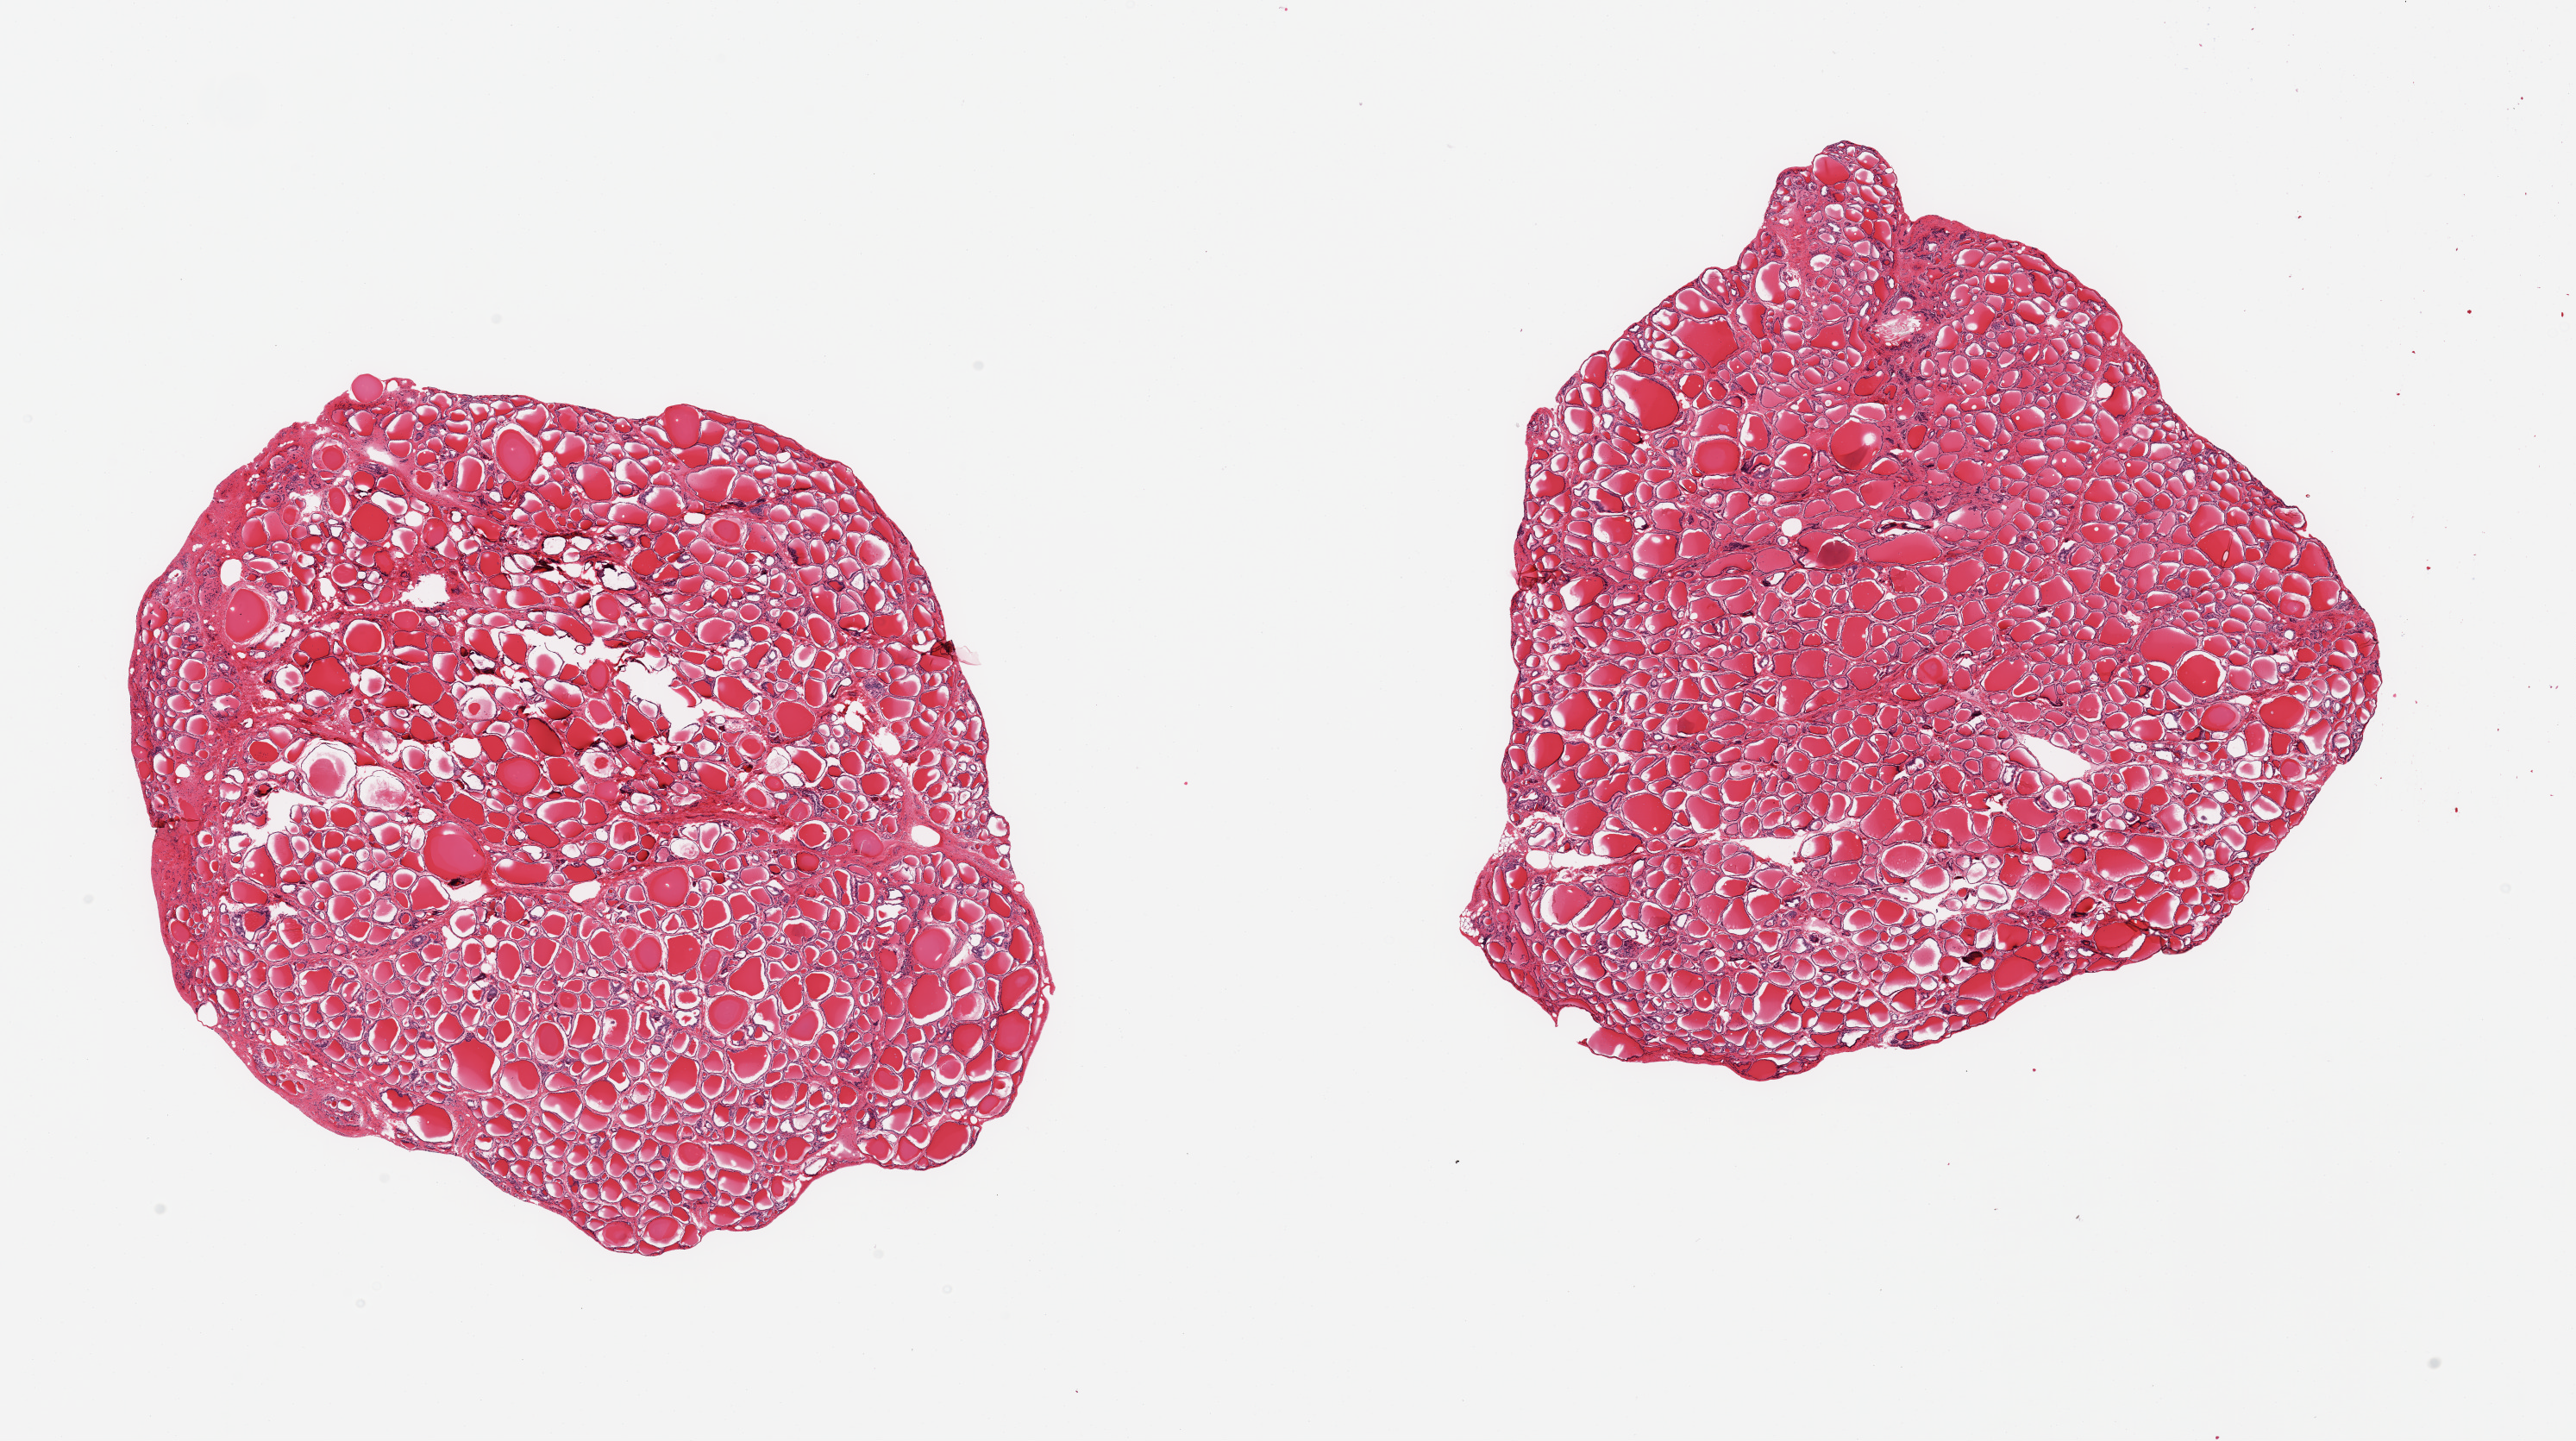
Whole-slide image, H&E stain — shown as a low-resolution overview of the whole scanned area (about 23.6 x 13.2 mm); PAXgene-fixed, paraffin-embedded tissue; target tissue: thyroid; donor tissue sample. Donor sex: male.
Review note (as recorded): 2 pieces.